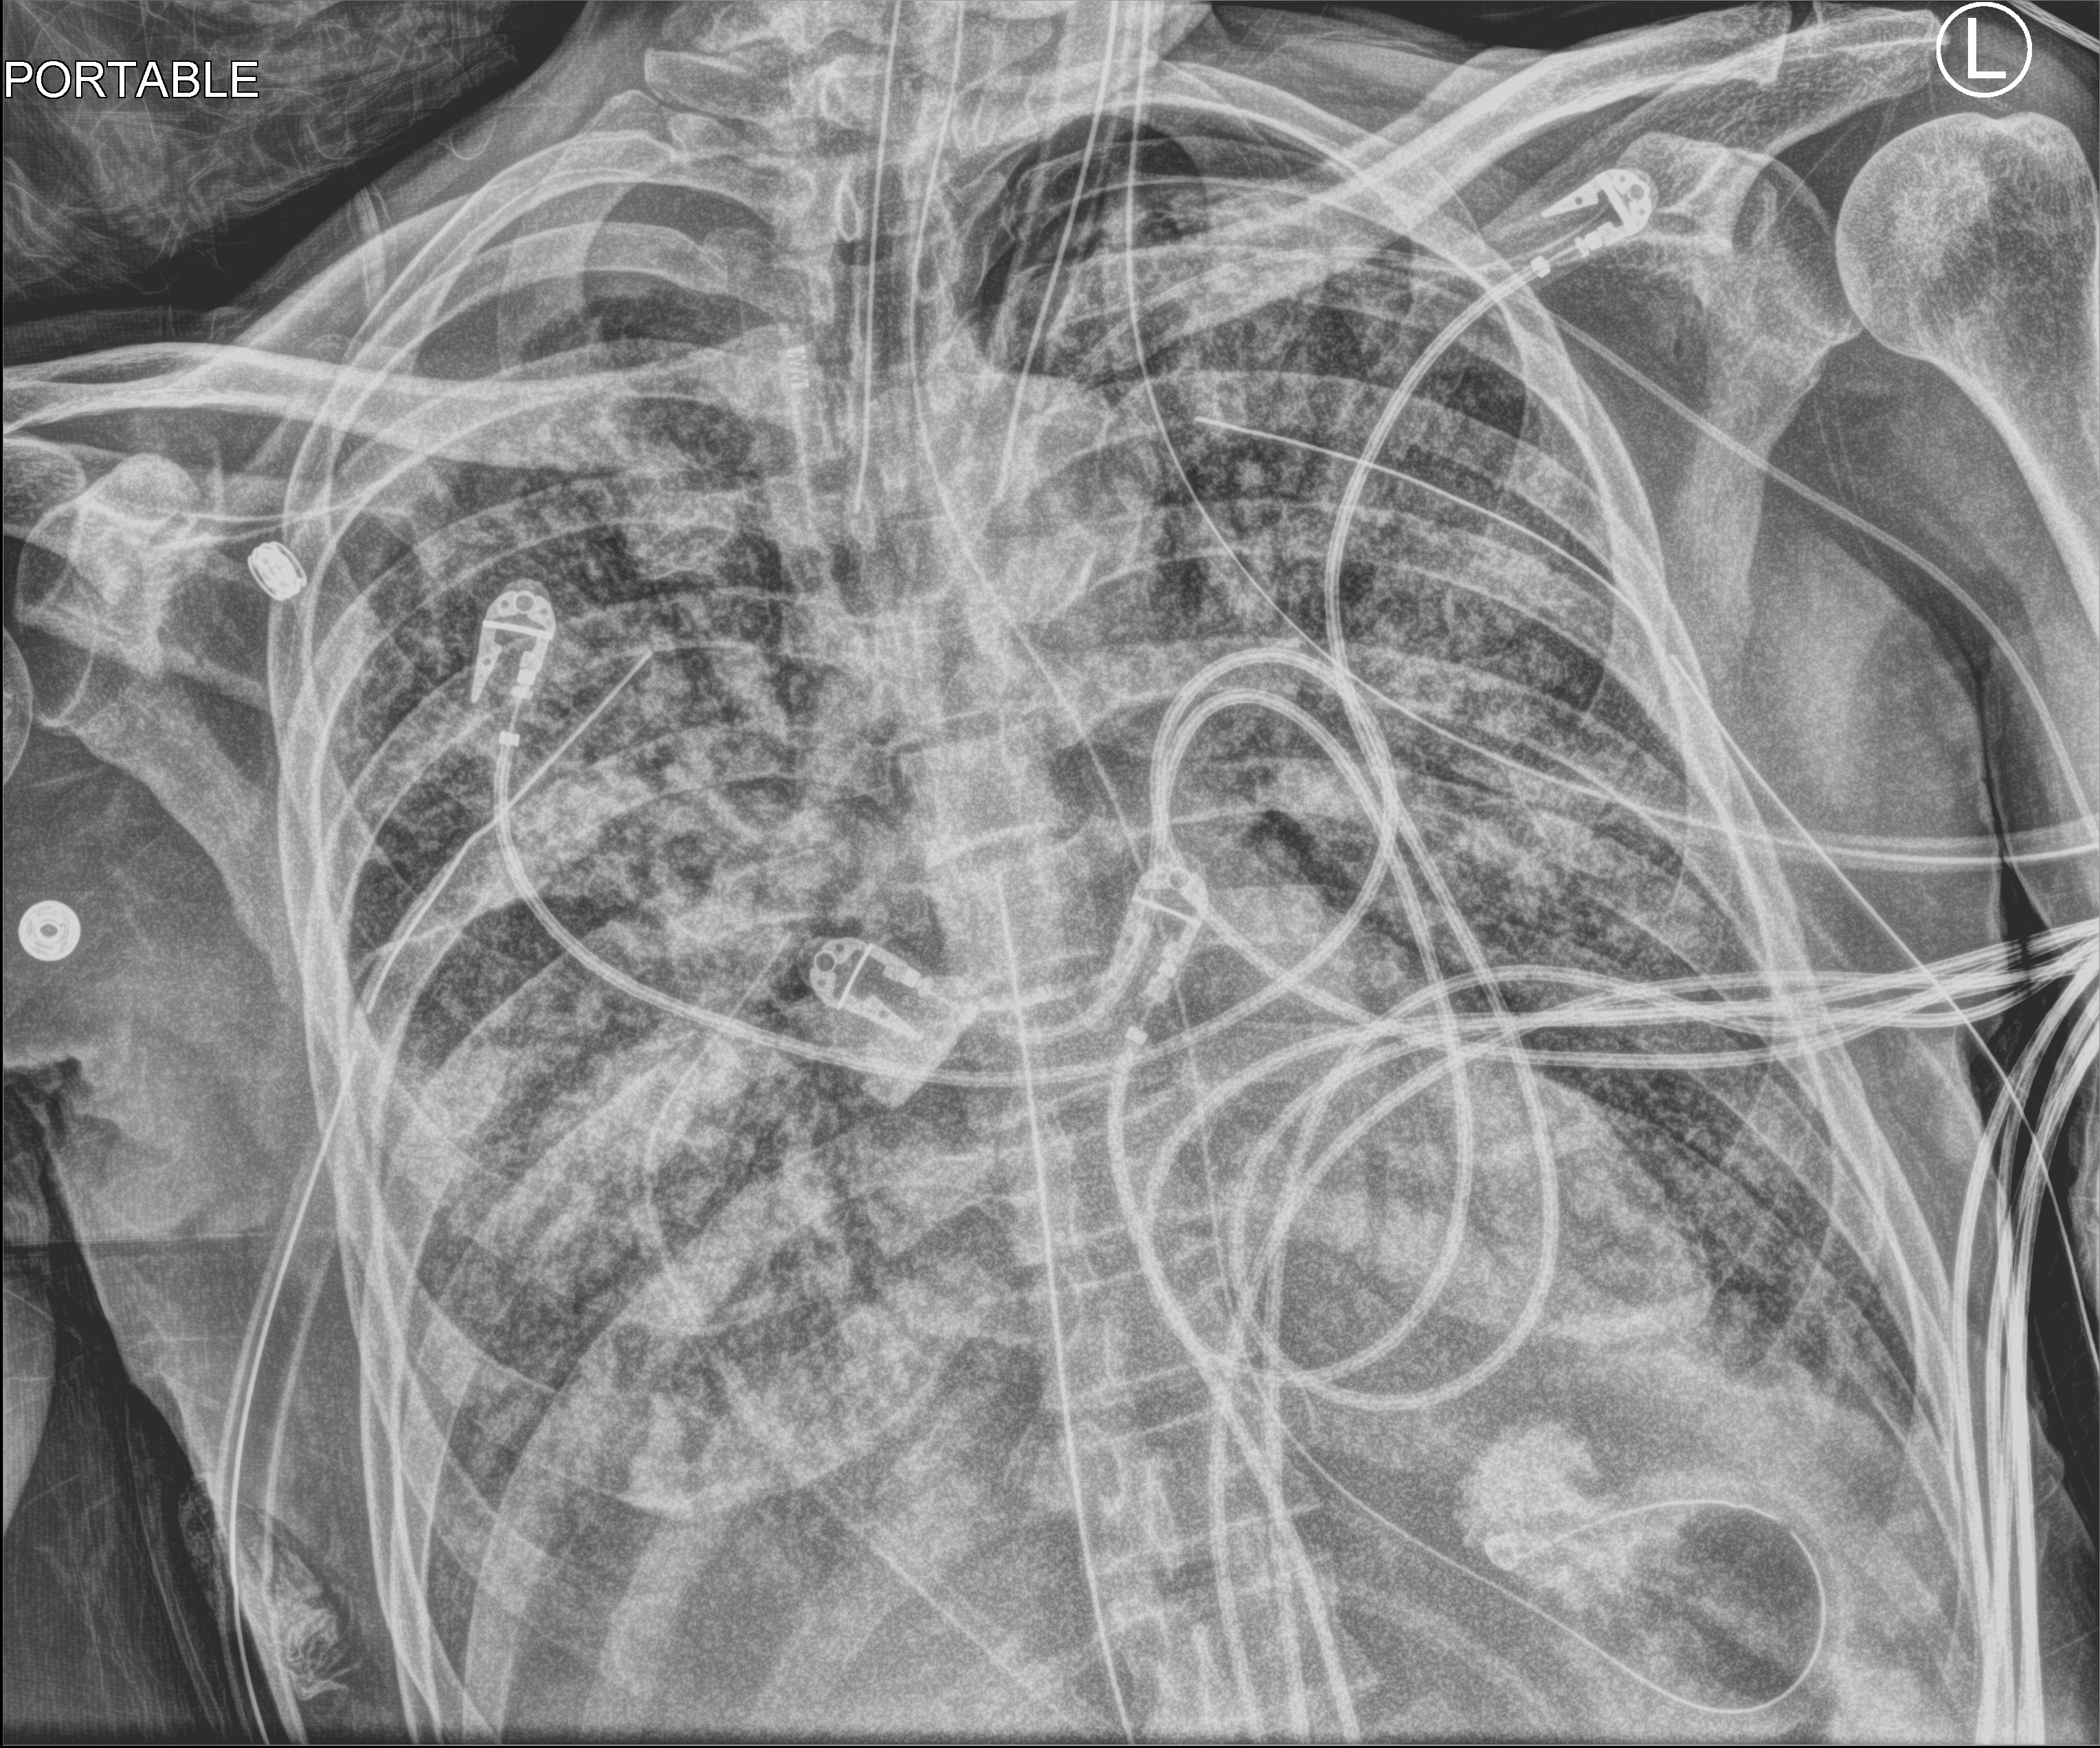
Chest X-ray (portable); anteroposterior (AP) projection. Patient hospitalised with COVID-19; male, aged 60–74 years.
Hospital-stay facts (about this admission, not read from this image; timing relative to this image not recorded): admitted to intensive care during this hospital stay: yes; mechanically ventilated during this hospital stay: yes.